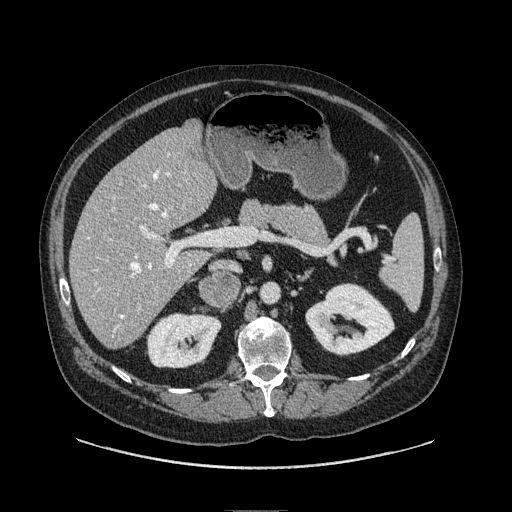
Contrast-enhanced abdominal CT, one axial slice. Slice 41 of 149 in the series (ordered by position). Soft-tissue window (W 400 / L 40 HU). 1.25 mm slice thickness. 512 × 512 image matrix, field of view 440 × 440 mm. Male patient. Case-level facts recorded for this patient, not image findings: diagnosis: adrenocortical carcinoma; tumour side: right adrenal; tumour size at pathology: 7.5 cm; Ki-67 index: 15 %; stage (as recorded): 2.
Outlined on this slice (semi-automatically segmented with operator editing):
- mass: bounding box [x1, y1, x2, y2] px = [203, 274, 237, 304]